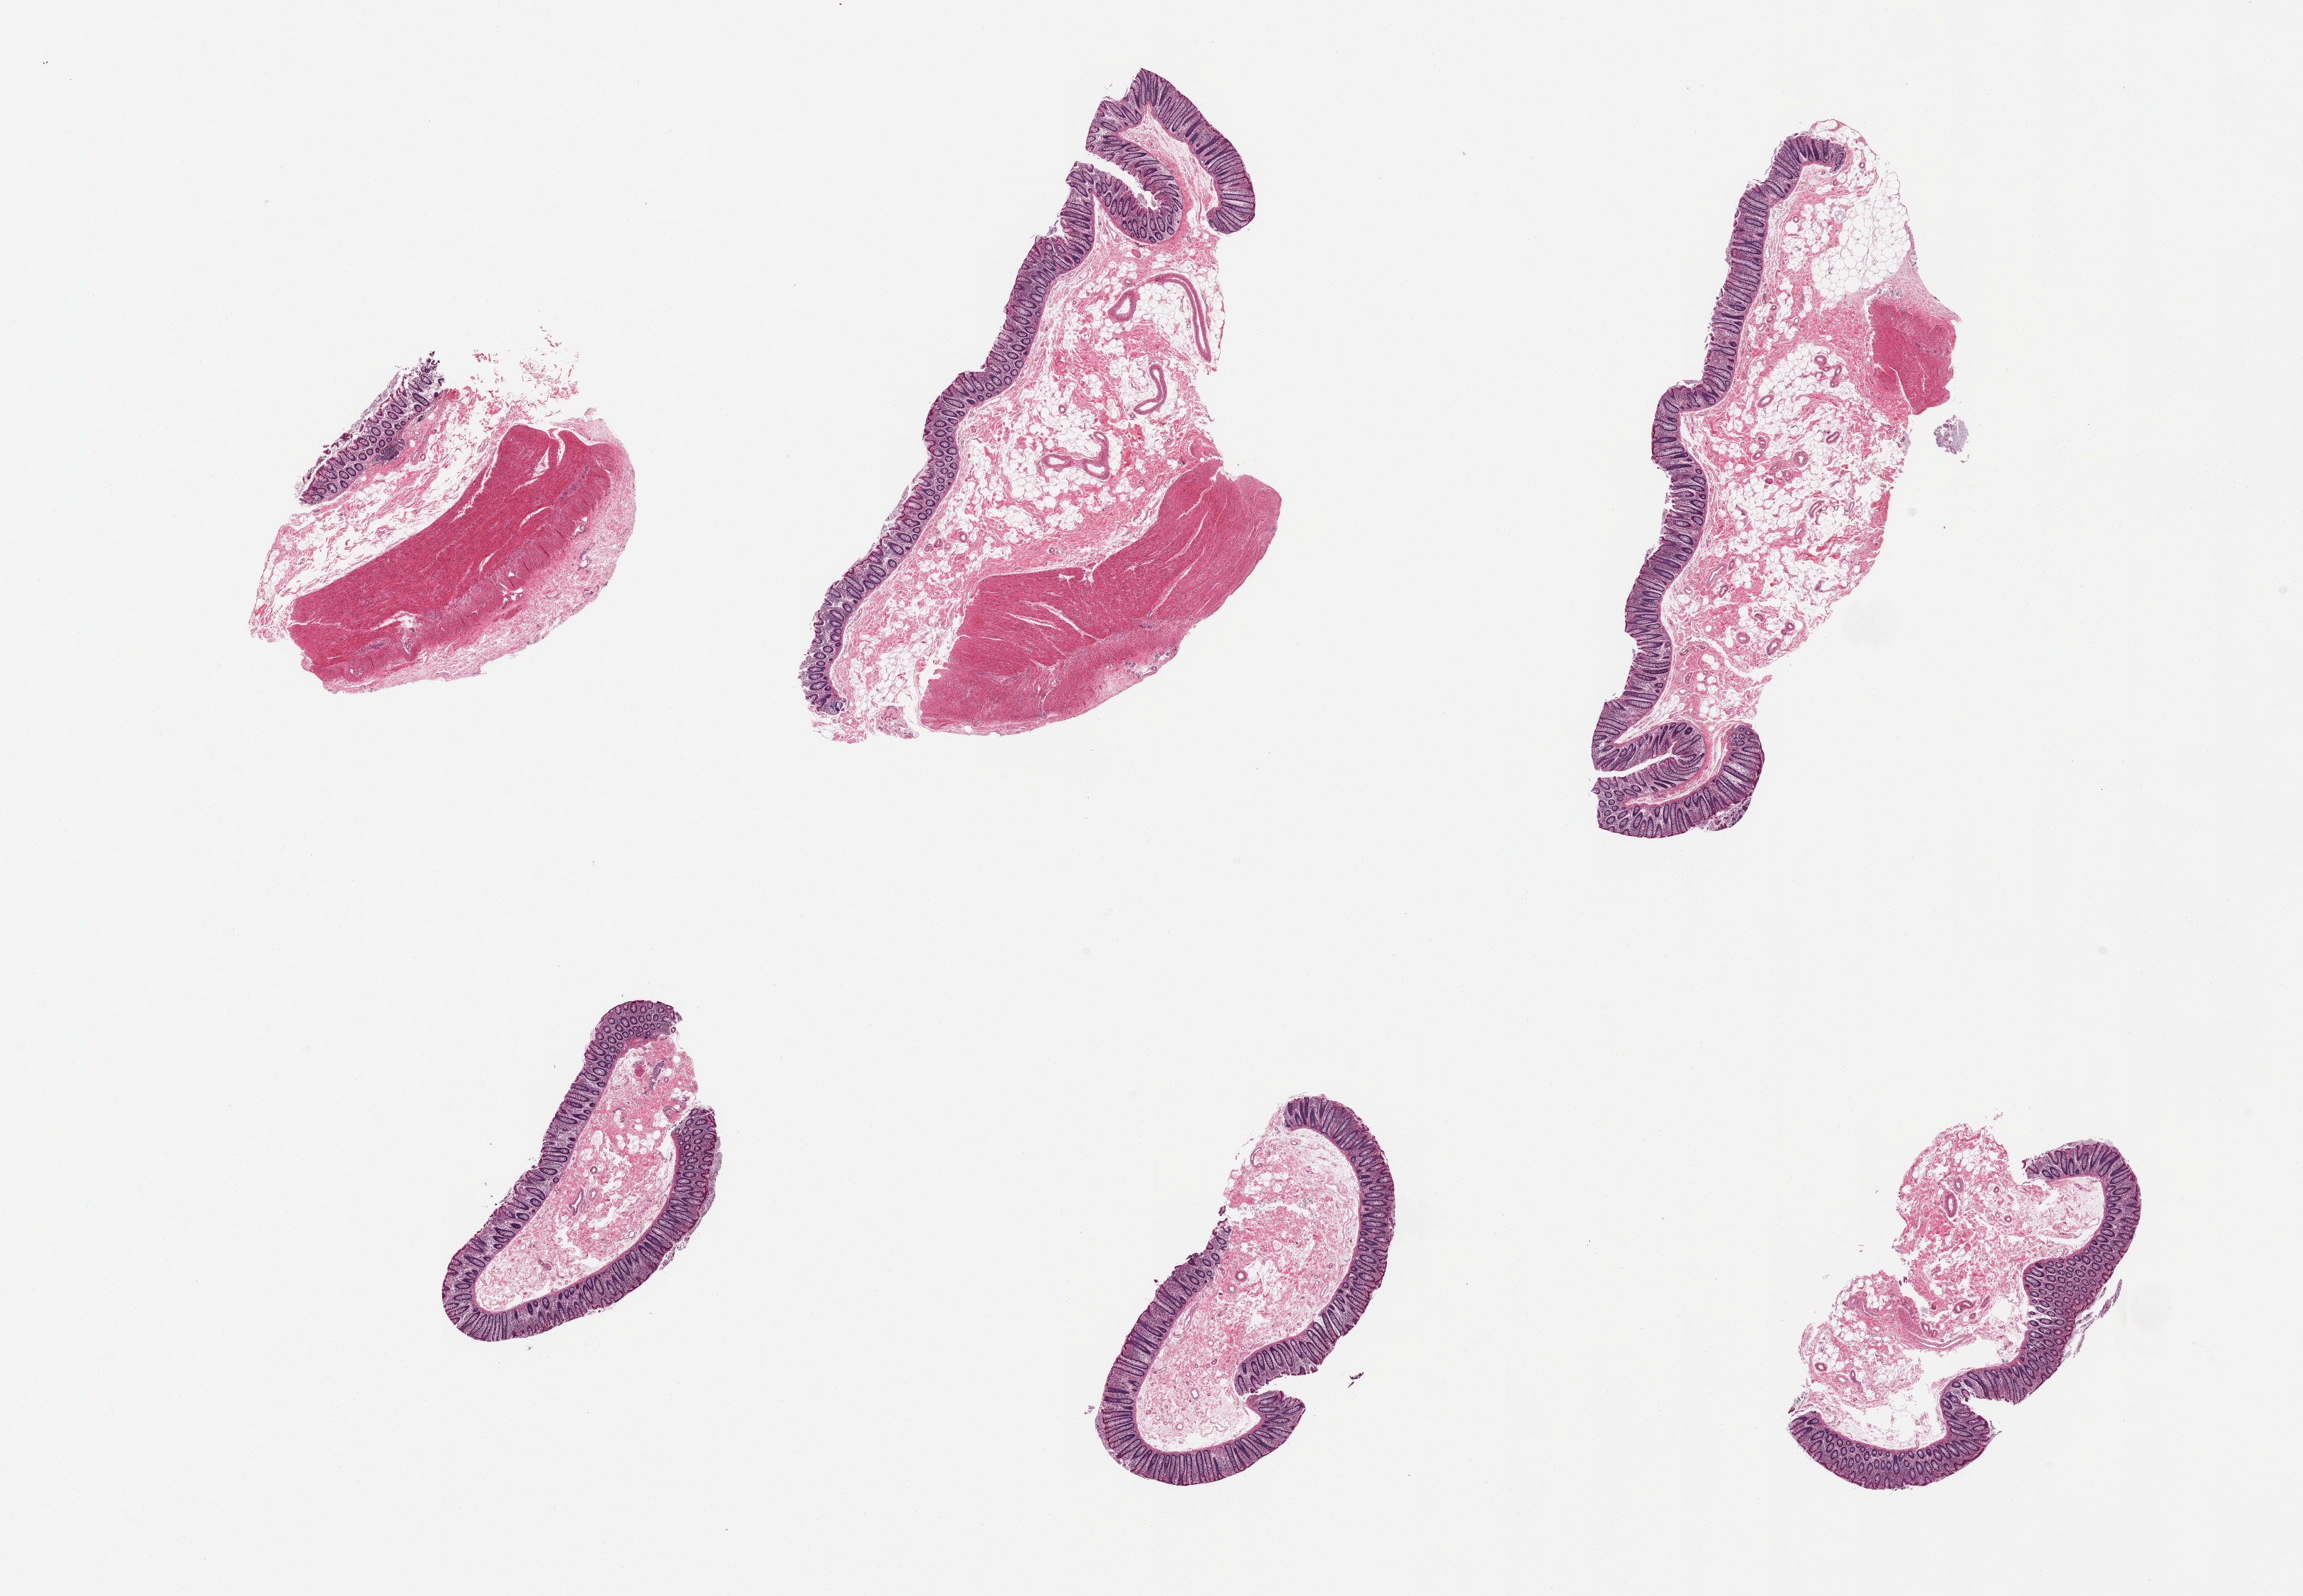
H&E whole-slide image, shown as a low-resolution overview of the whole scanned area (about 25.6 x 17.7 mm); PAXgene-fixed, paraffin-embedded tissue; sampled site (target tissue): transverse colon; tissue donor sample. Donor sex: male.
Reviewer comment on this tissue sample: 6 pieces; mostly well preserved mucosa and submucosa, 3 of 6 contain muscularis.